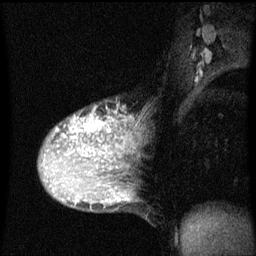
Breast MRI (dynamic contrast-enhanced), one sagittal slice. Slice 36 of 60 in the series (ordered by position). Dynamic contrast-enhanced series, image 2 of 3 at this slice position (ordered by acquisition). 1.5 T. TE 4.2 ms, TR 8 ms. 2 mm slice thickness. 256 × 256 image matrix, field of view 200 × 200 mm. Female patient, age 36 years.
Annotated regions visible in this slice (semi-automatically segmented with operator editing):
- analysis volume of interest (the breast-tissue region the enhancement analysis was run in; not a lesion): bounding box (x1, y1, x2, y2) in pixels: (39, 106, 122, 169)
- tumour enhancement mask (voxels above the 70 % enhancement threshold inside the analysis volume of interest): (56, 108, 119, 169)